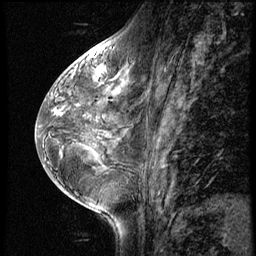
Breast MRI (dynamic contrast-enhanced), one sagittal slice; position 26 of 56 along the scan axis; 3 images stored at this slice position (order not interpretable as contrast timing); 1.5 T; TE 4.2 ms, TR 8.9 ms; 2.5 mm slice thickness; 256 × 256 image matrix, field of view 200 × 200 mm. Patient: female, 38 years. From the clinical record (not read from this slice): setting: breast cancer imaged before/during neoadjuvant chemotherapy; receptor status: triple-negative.
Annotated regions visible in this slice (semi-automatically segmented with operator editing):
- analysis volume of interest (the breast-tissue region the enhancement analysis was run in; not a lesion): box from (x=88, y=60) to (x=110, y=84) px
- tumour enhancement mask (voxels above the 140 % enhancement threshold inside the analysis volume of interest): (x=98, y=68)–(x=105, y=72)